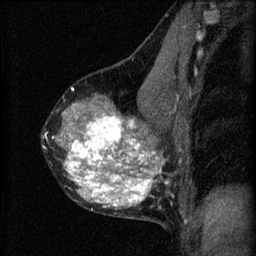
Breast MRI (dynamic contrast-enhanced), one sagittal slice; slice 37 of 60 in the series (ordered by position); 3 images stored at this slice position (order not interpretable as contrast timing); 1.5 T; TE 4.2 ms, TR 8.2 ms; 2 mm slice thickness; 256 × 256 image matrix, field of view 180 × 180 mm. Female patient, age 40 years.
Structures marked on this image (semi-automatic segmentation, software-assisted and operator-edited):
- analysis volume of interest (the breast-tissue region the enhancement analysis was run in; not a lesion): bounding box [x1, y1, x2, y2] px = [42, 76, 179, 219]
- tumour enhancement mask (voxels above the 70 % enhancement threshold inside the analysis volume of interest): [46, 114, 165, 209]